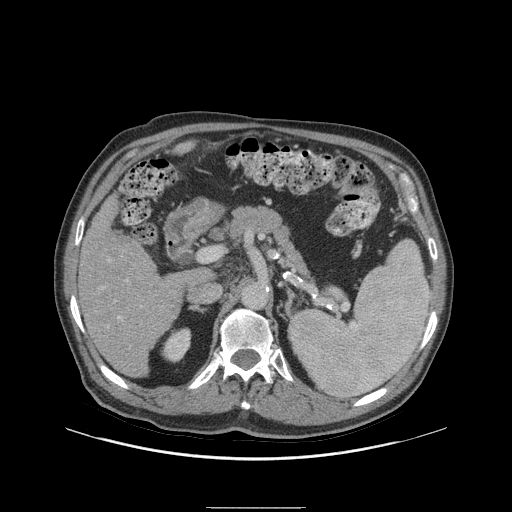
Contrast-enhanced abdominal CT (liver protocol), one axial slice; position 49 of 105 along the scan axis; reconstruction kernel STANDARD; 140 kVp; soft-tissue window (W 400 / L 40 HU); 2.5 mm slice thickness; 512 × 512 image matrix. Case-level facts recorded for this patient, not image findings: diagnosis: hepatocellular carcinoma (patient treated with transarterial chemoembolisation; whether this scan precedes or follows treatment is not stated here); TNM stage (as recorded): Stage-I; Child-Pugh class: A; tumour nodularity: uninodular; tumour size: 5.1 cm.
Annotated regions visible in this slice (semi-automatic segmentation, software-assisted and operator-edited):
- liver parenchyma outside the tumour (the mass and vessels are separate outlines, so this box may not span the whole liver): bounding box (x1, y1, x2, y2) in pixels: (78, 195, 190, 378)
- liver vessels: (102, 260, 121, 319)